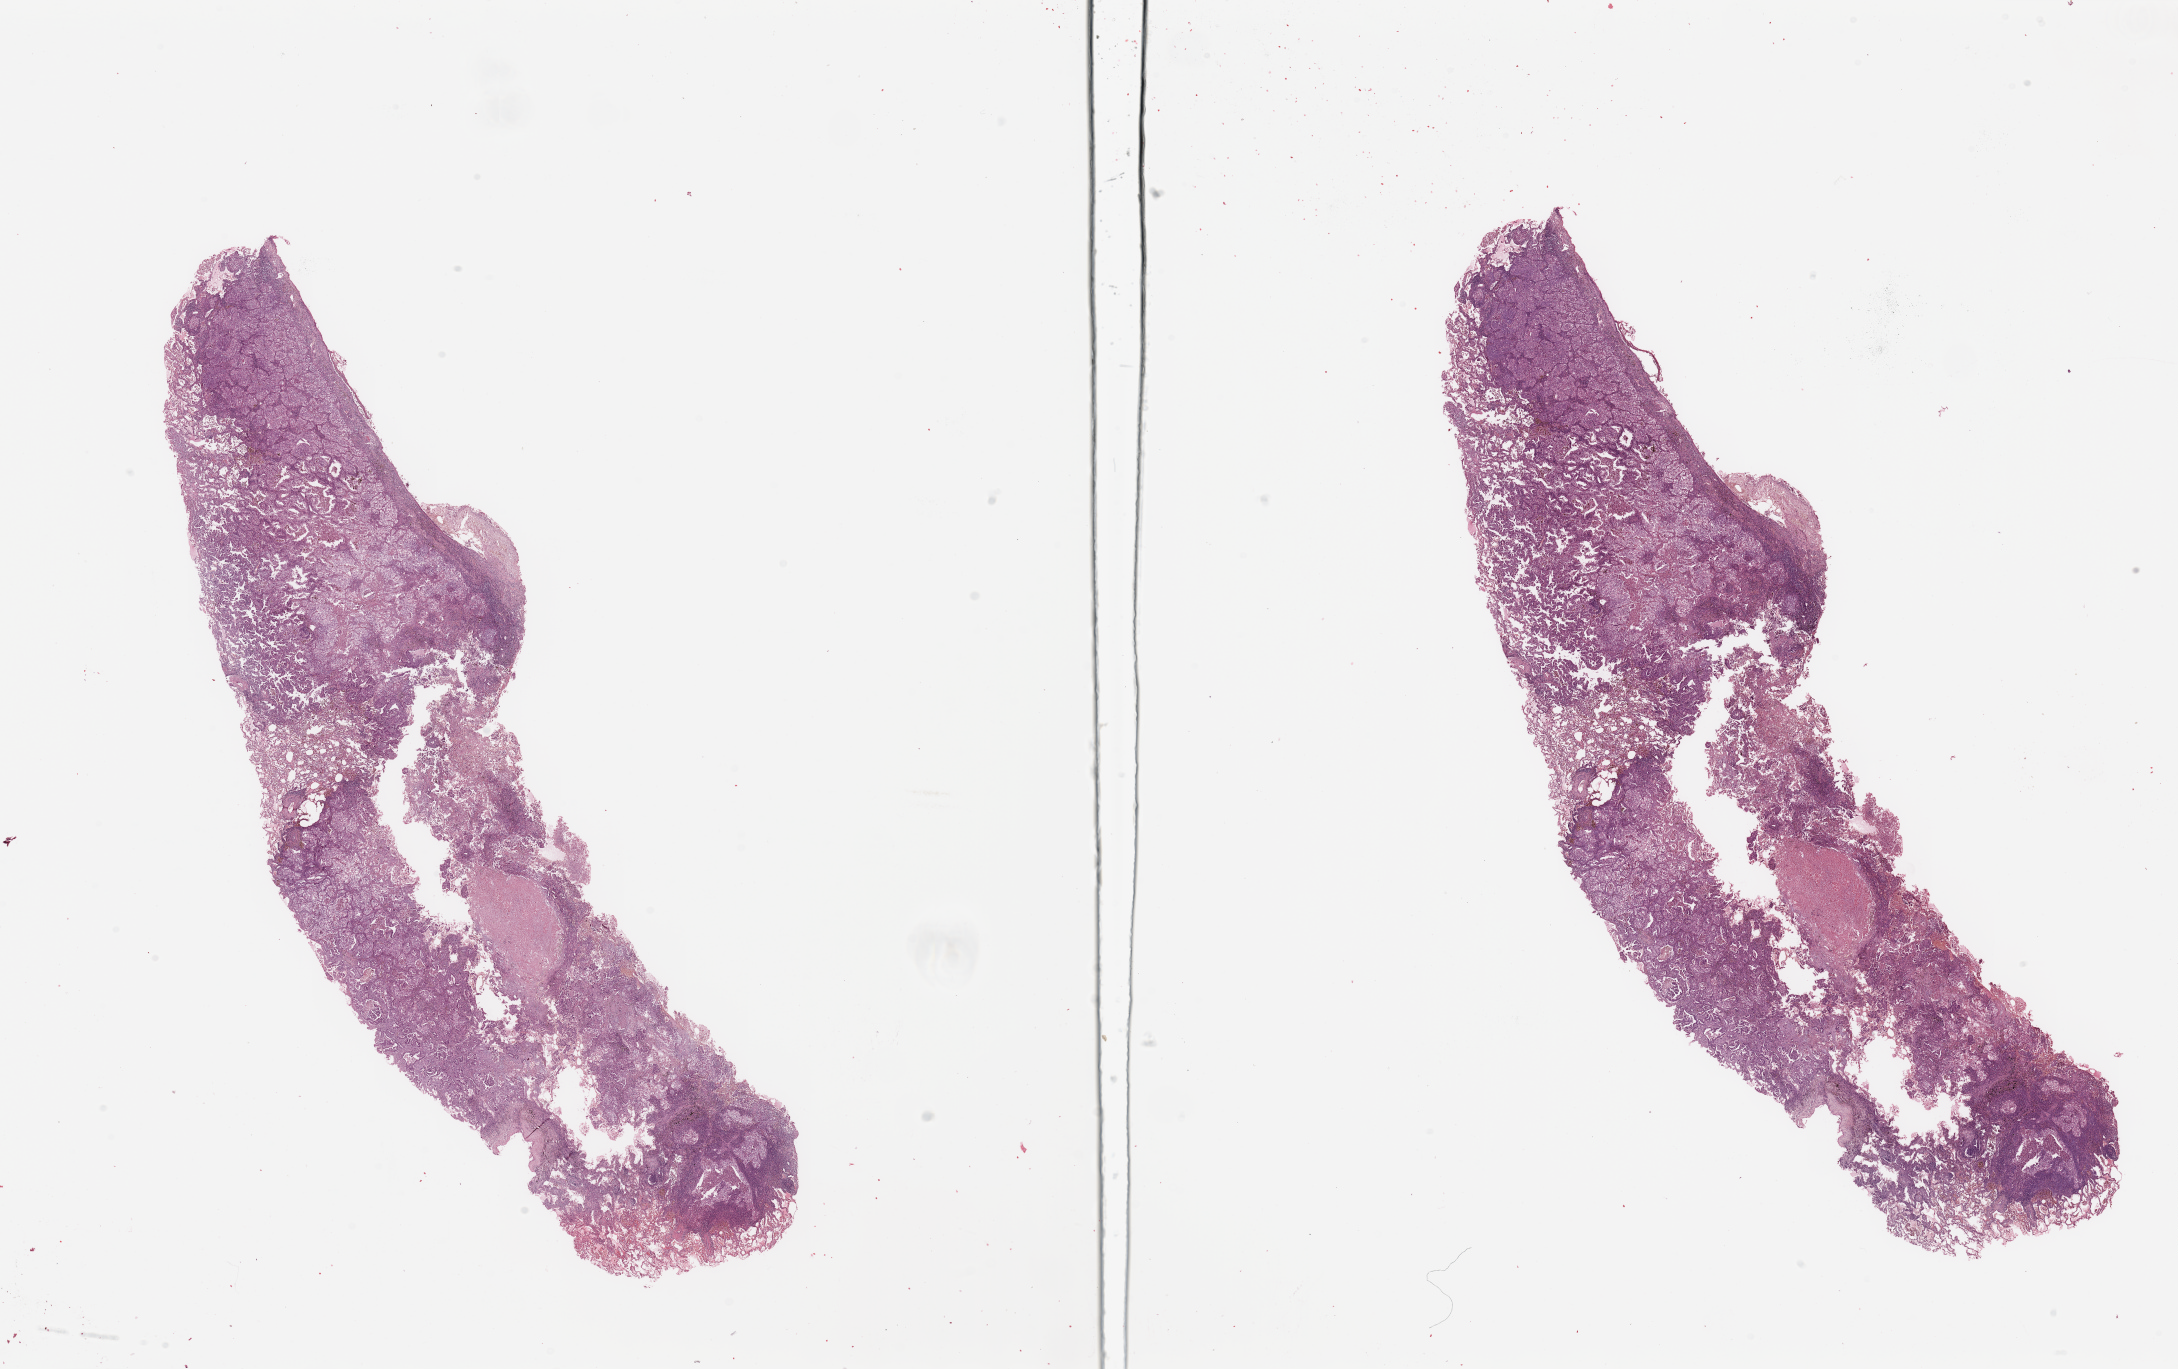
Whole-slide histology image, H&E-stained, a low-resolution overview of the entire scanned area, about 34.5 x 21.7 mm (from a 20x scan), tumour tissue sample, lung. Male, 51 y/o.
Histologic diagnosis: Adenocarcinoma, NOS.